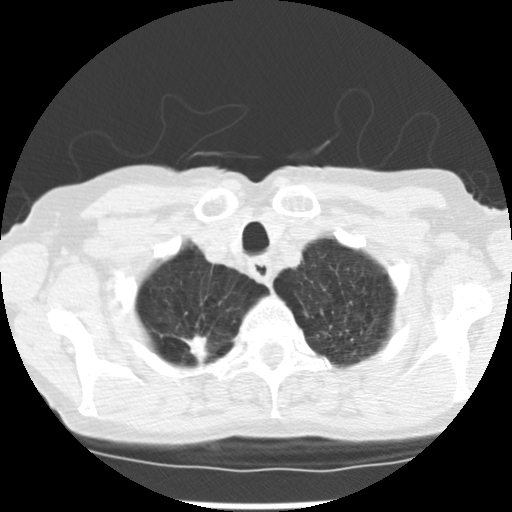
Chest CT (low-dose screening protocol), one axial image; baseline annual screen; lung window (W 1500 / L -600 HU); 2.5 mm slice thickness; 120 kVp; slice 23 of 265 in the series. Female participant, aged 72 years at enrolment. Current smoker at enrolment.
Expert-annotated lung lesion, bounding box <168,316,231,362> (left, top, right, bottom; pixels). The screening reader recorded 3 non-calcified nodules or masses ≥4 mm on this exam (right upper lobe, left upper lobe, left lower lobe); which of them this box marks is not recorded. Participant outcome: lung cancer diagnosed 50 days after this screen — adenocarcinoma, NOS, right upper lobe, moderately differentiated (G2), stage IB (AJCC 6th edition), 22 mm at pathology.